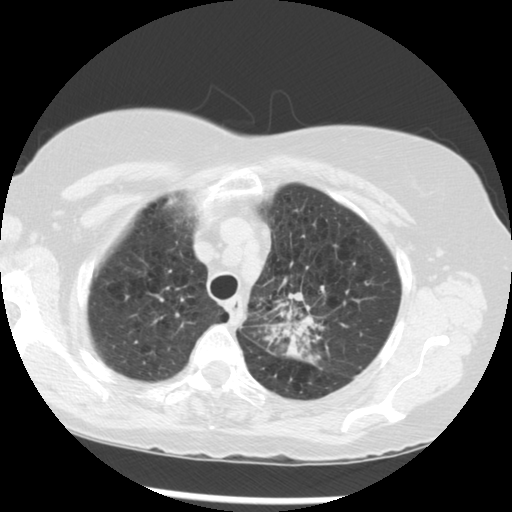
Low-dose screening chest CT, axial slice; third annual screen; lung window (W 1500 / L -600 HU); 2.5 mm slice thickness; standard (soft-tissue) reconstruction kernel (STANDARD); 120 kVp. Female participant, aged 70 years at enrolment.
Expert reader's lesion annotation, bounding box [x1, y1, x2, y2] px = [257, 279, 353, 368]. Reader record for this screening exam (exam-level; its link to the box is not recorded): non-calcified nodule or mass ≥4 mm, left upper lobe, 32 × 26 mm, spiculated (stellate) margins, soft tissue attenuation, pre-existing on the prior screen: yes; interval growth: yes. Lung cancer was diagnosed 24 days after this screen: neoplasm, malignant, left upper lobe, stage IIIB (AJCC 6th edition), 40 mm at pathology.